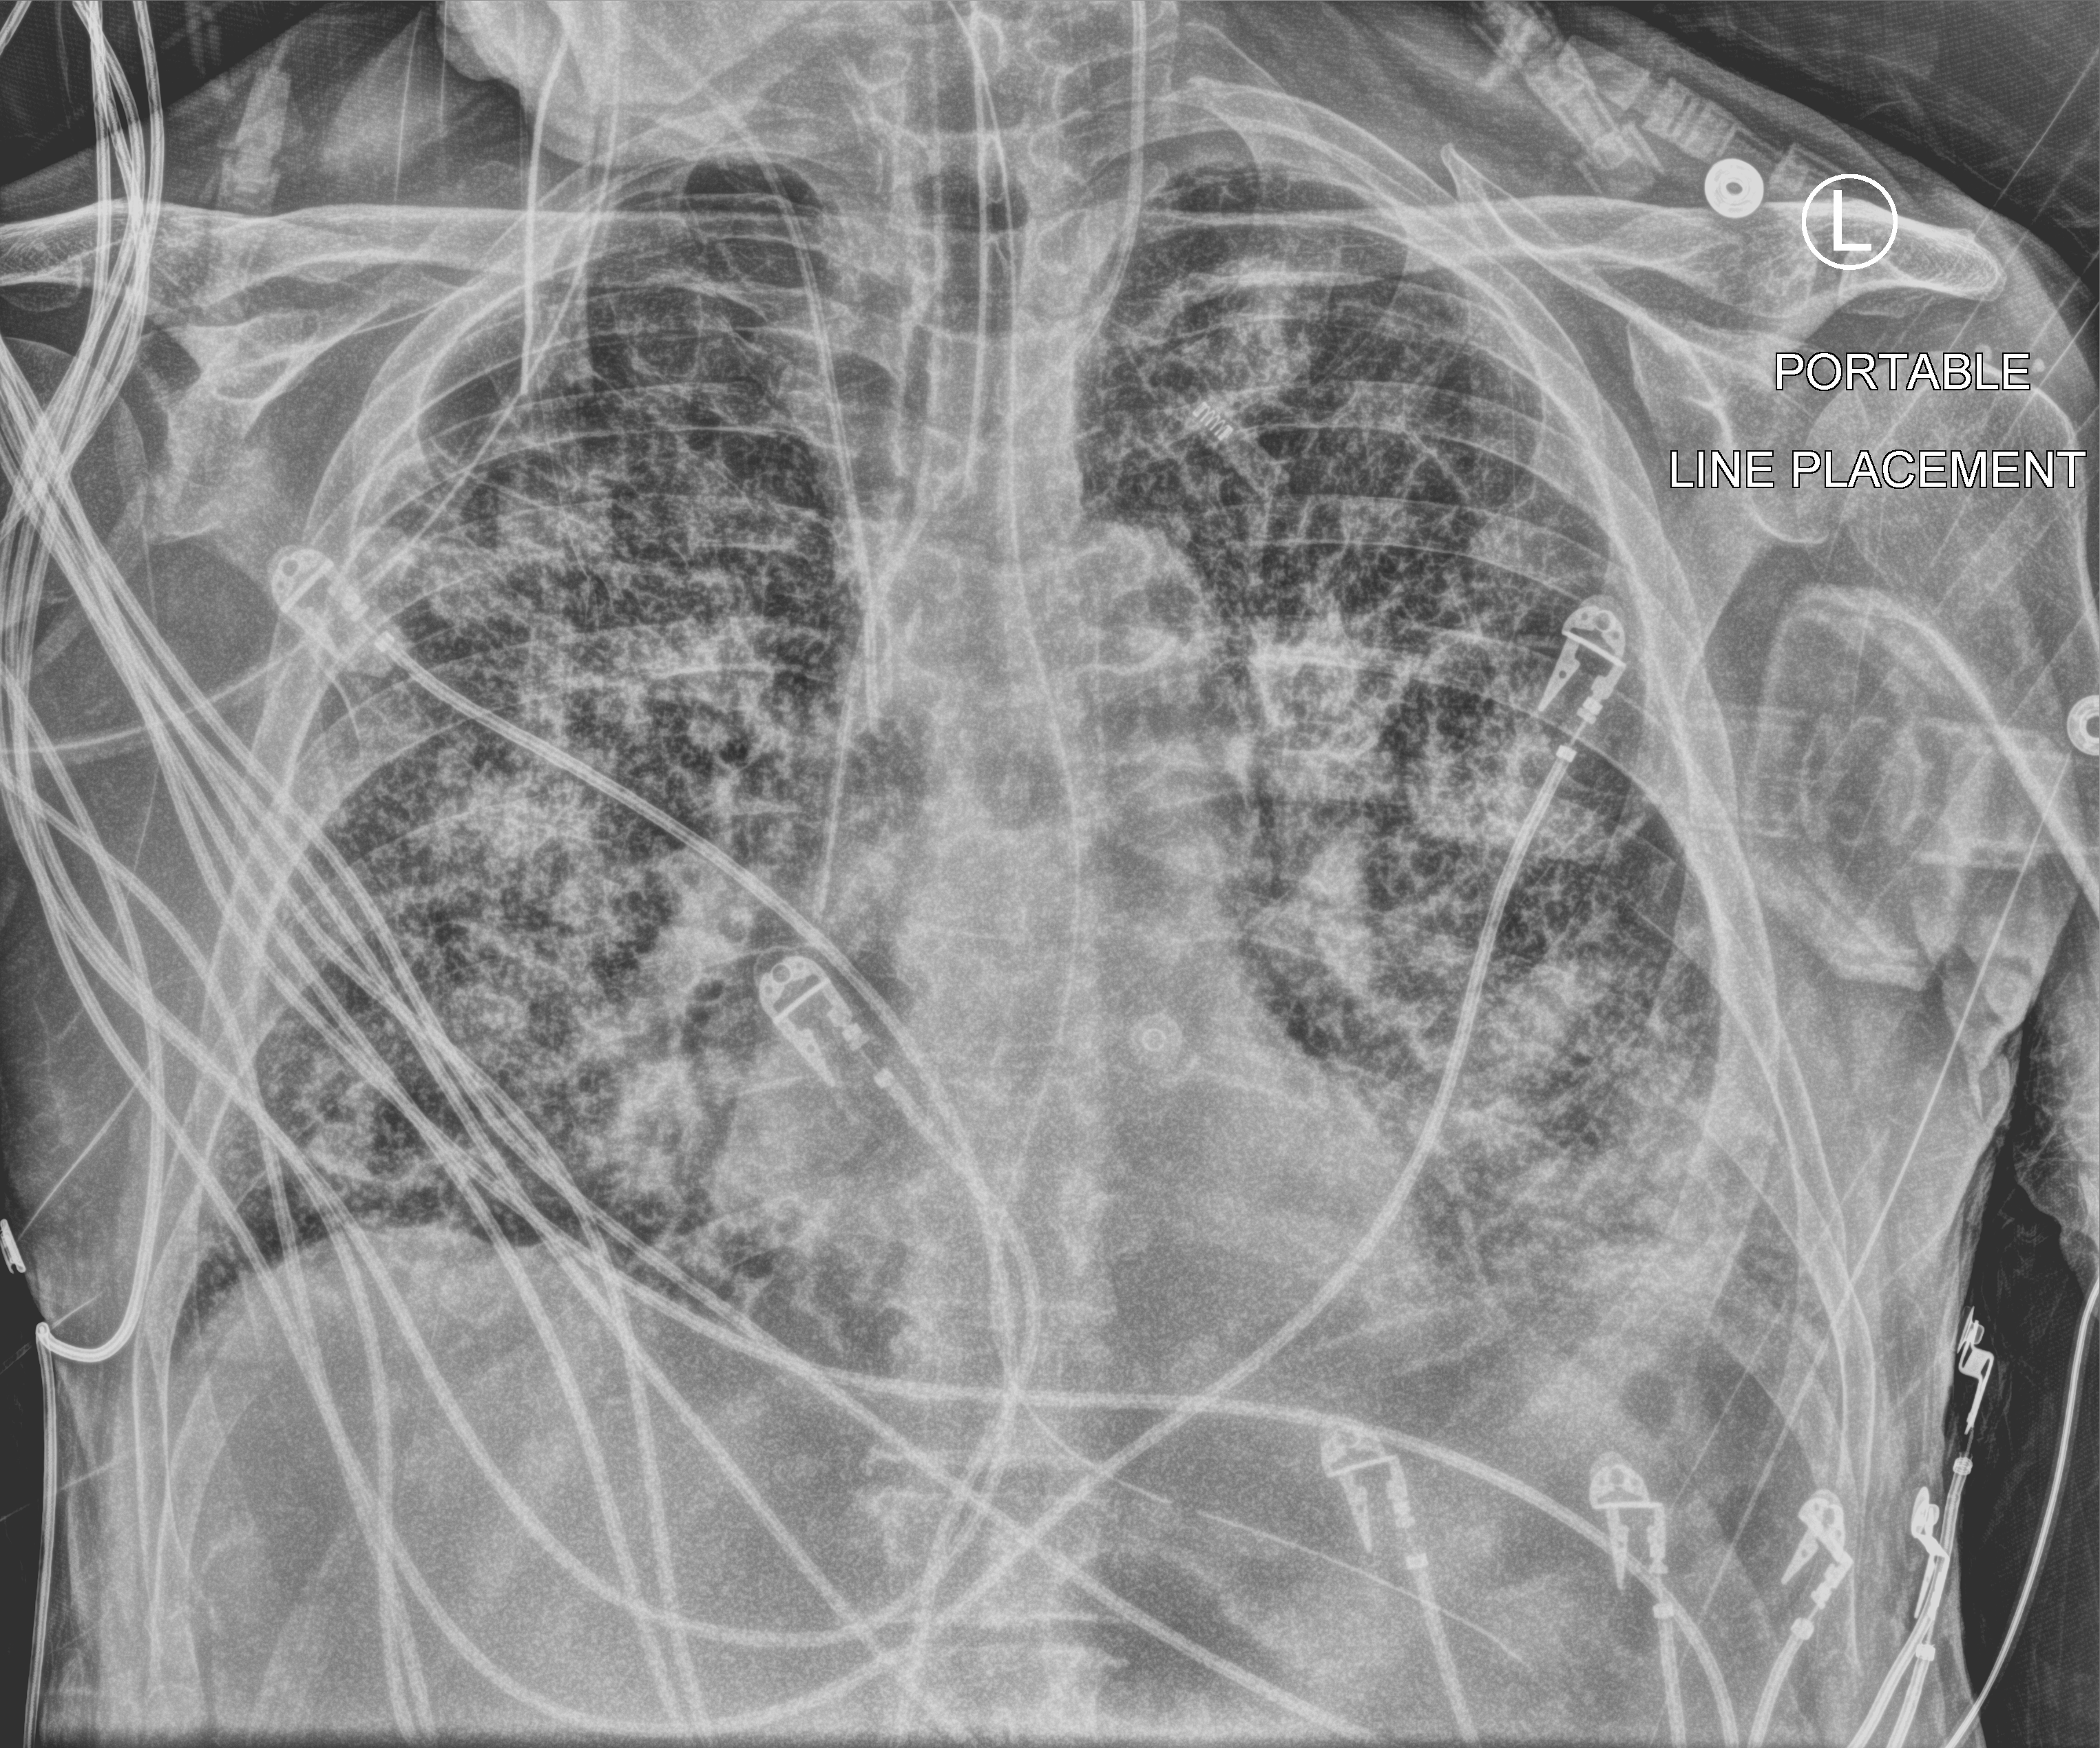
Portable chest radiograph, anteroposterior (AP) projection. Patient hospitalised with COVID-19; male, aged 75–90 years.
Admission-level facts for this patient (not findings on this image; timing relative to this image not recorded): length of hospital stay: 13 days; smoking status (admission record): never; admitted to intensive care during this hospital stay: yes.